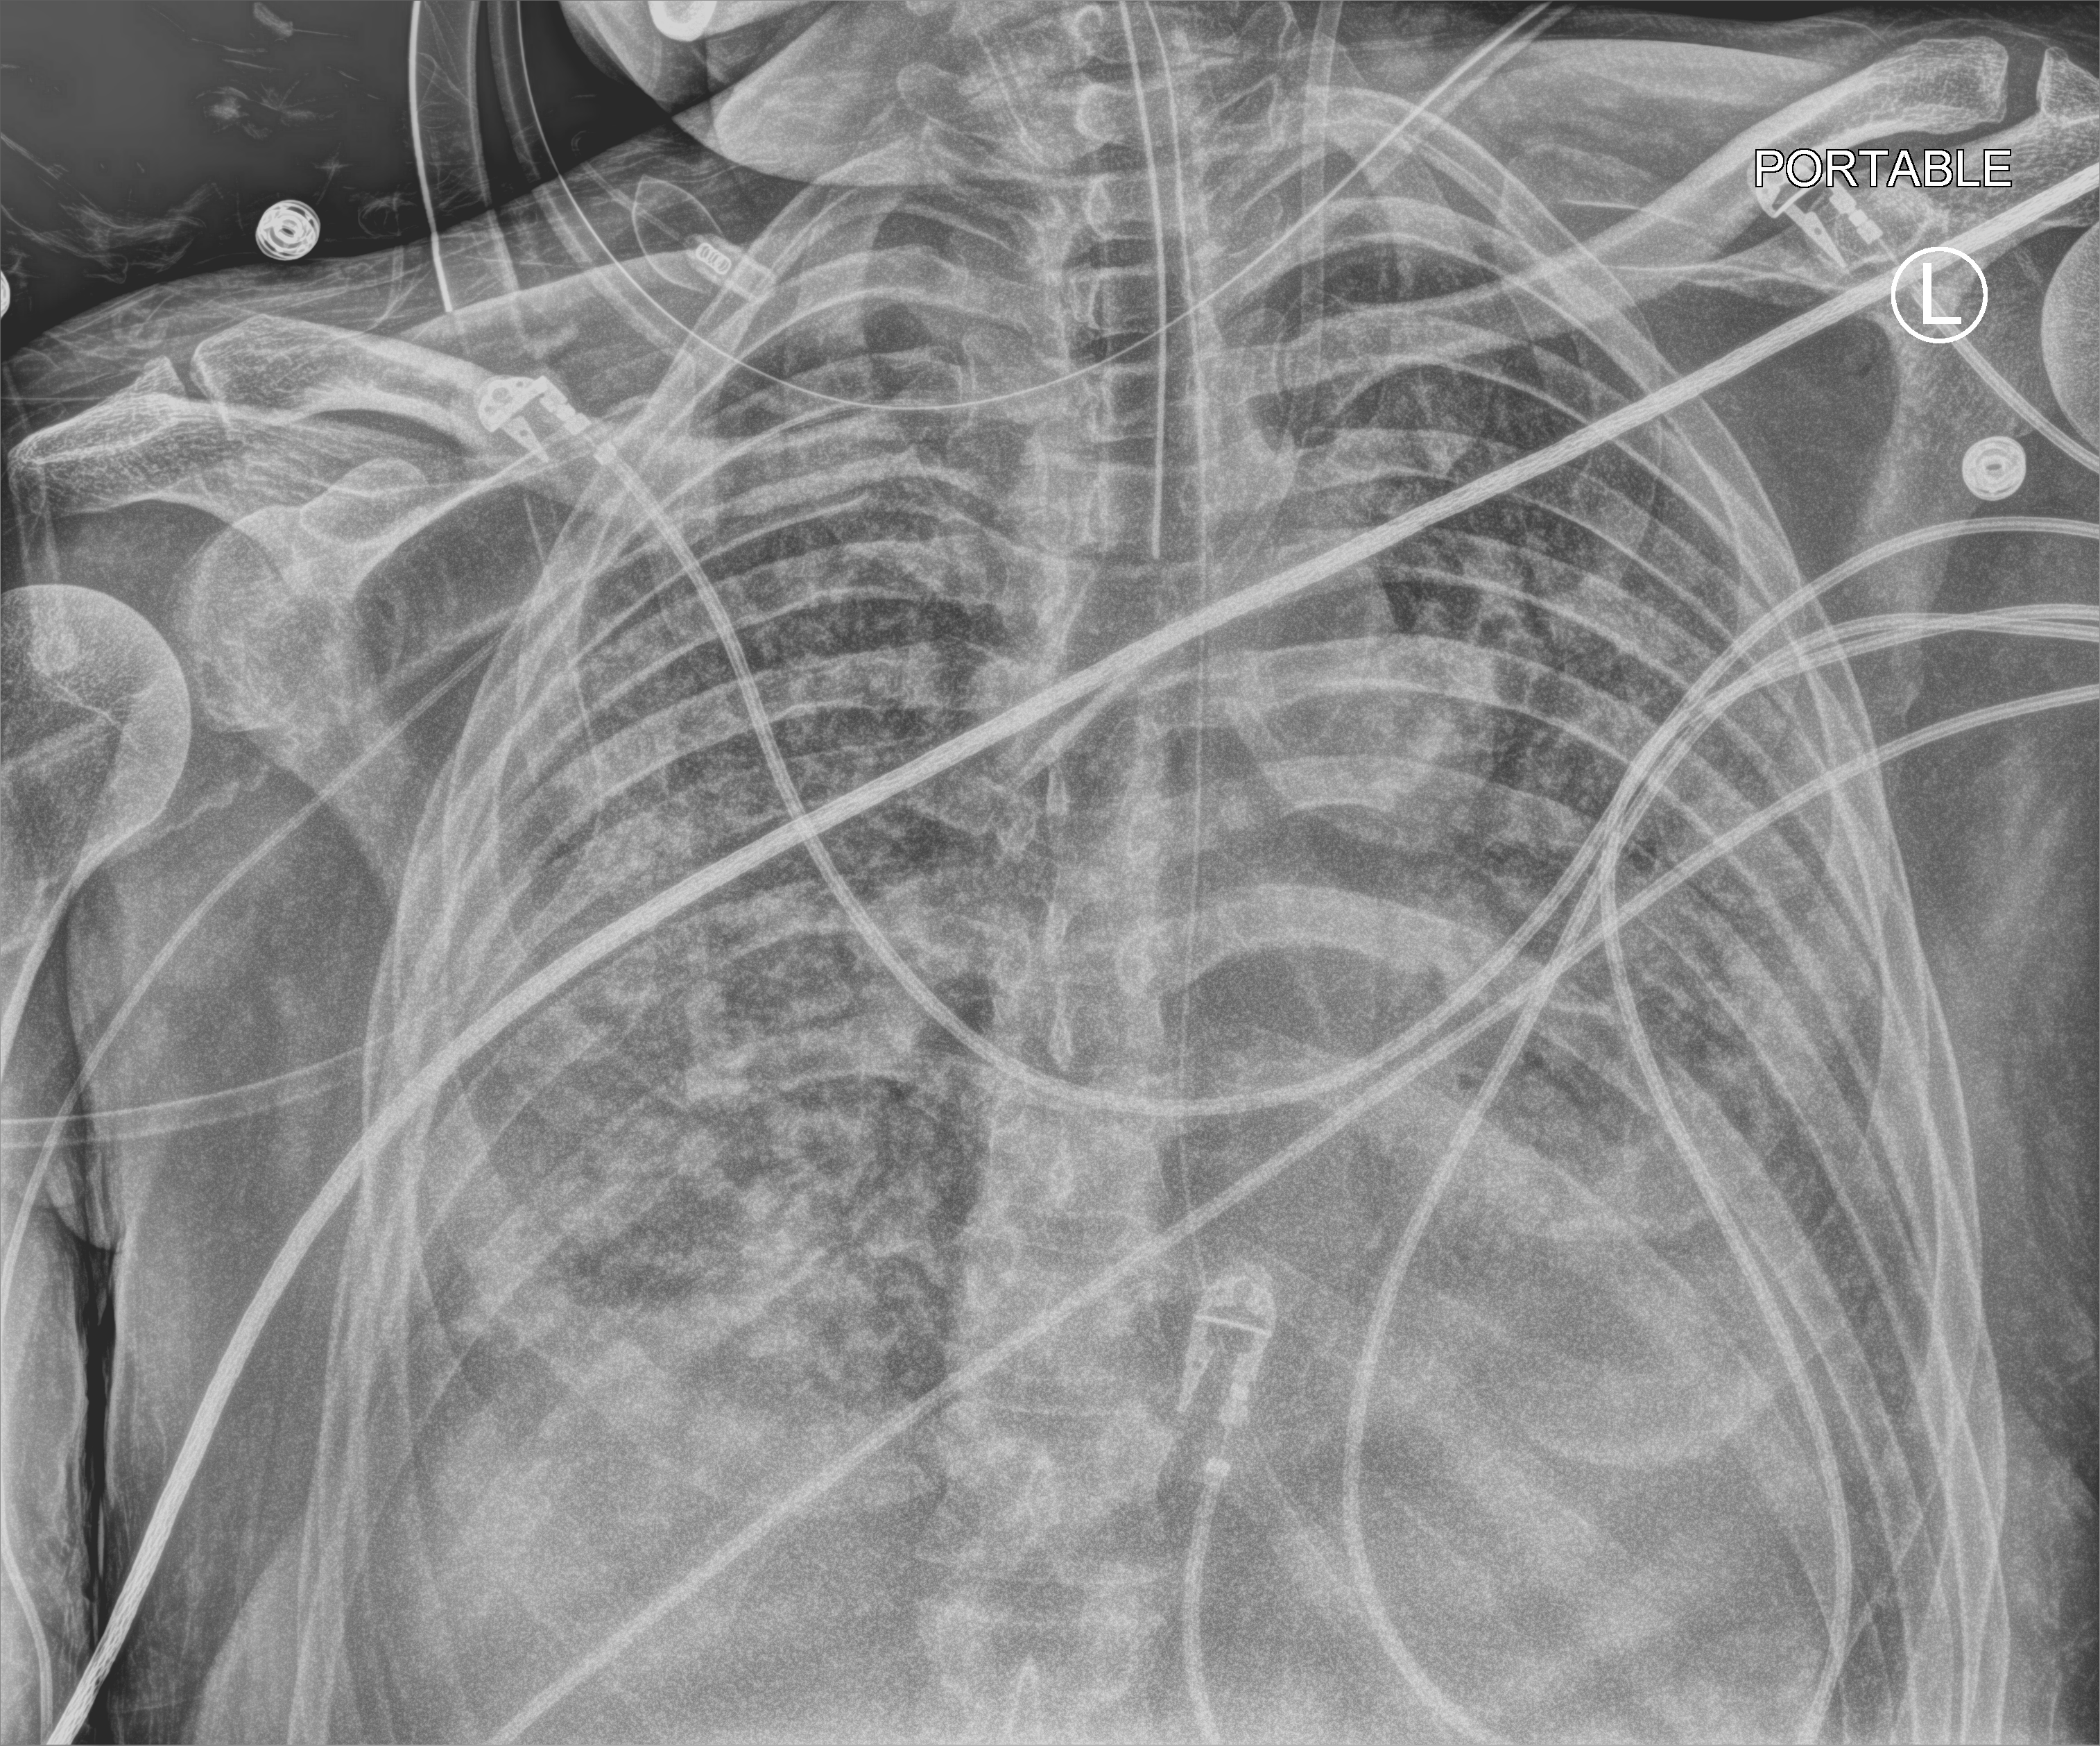
Bedside chest radiograph (computed radiography); anteroposterior (AP) projection. Male patient hospitalised with COVID-19, age 18–59 years.
Admission-level facts for this patient (not findings on this image; timing relative to this image not recorded): admitted to intensive care during this hospital stay: yes; mechanically ventilated during this hospital stay: yes.